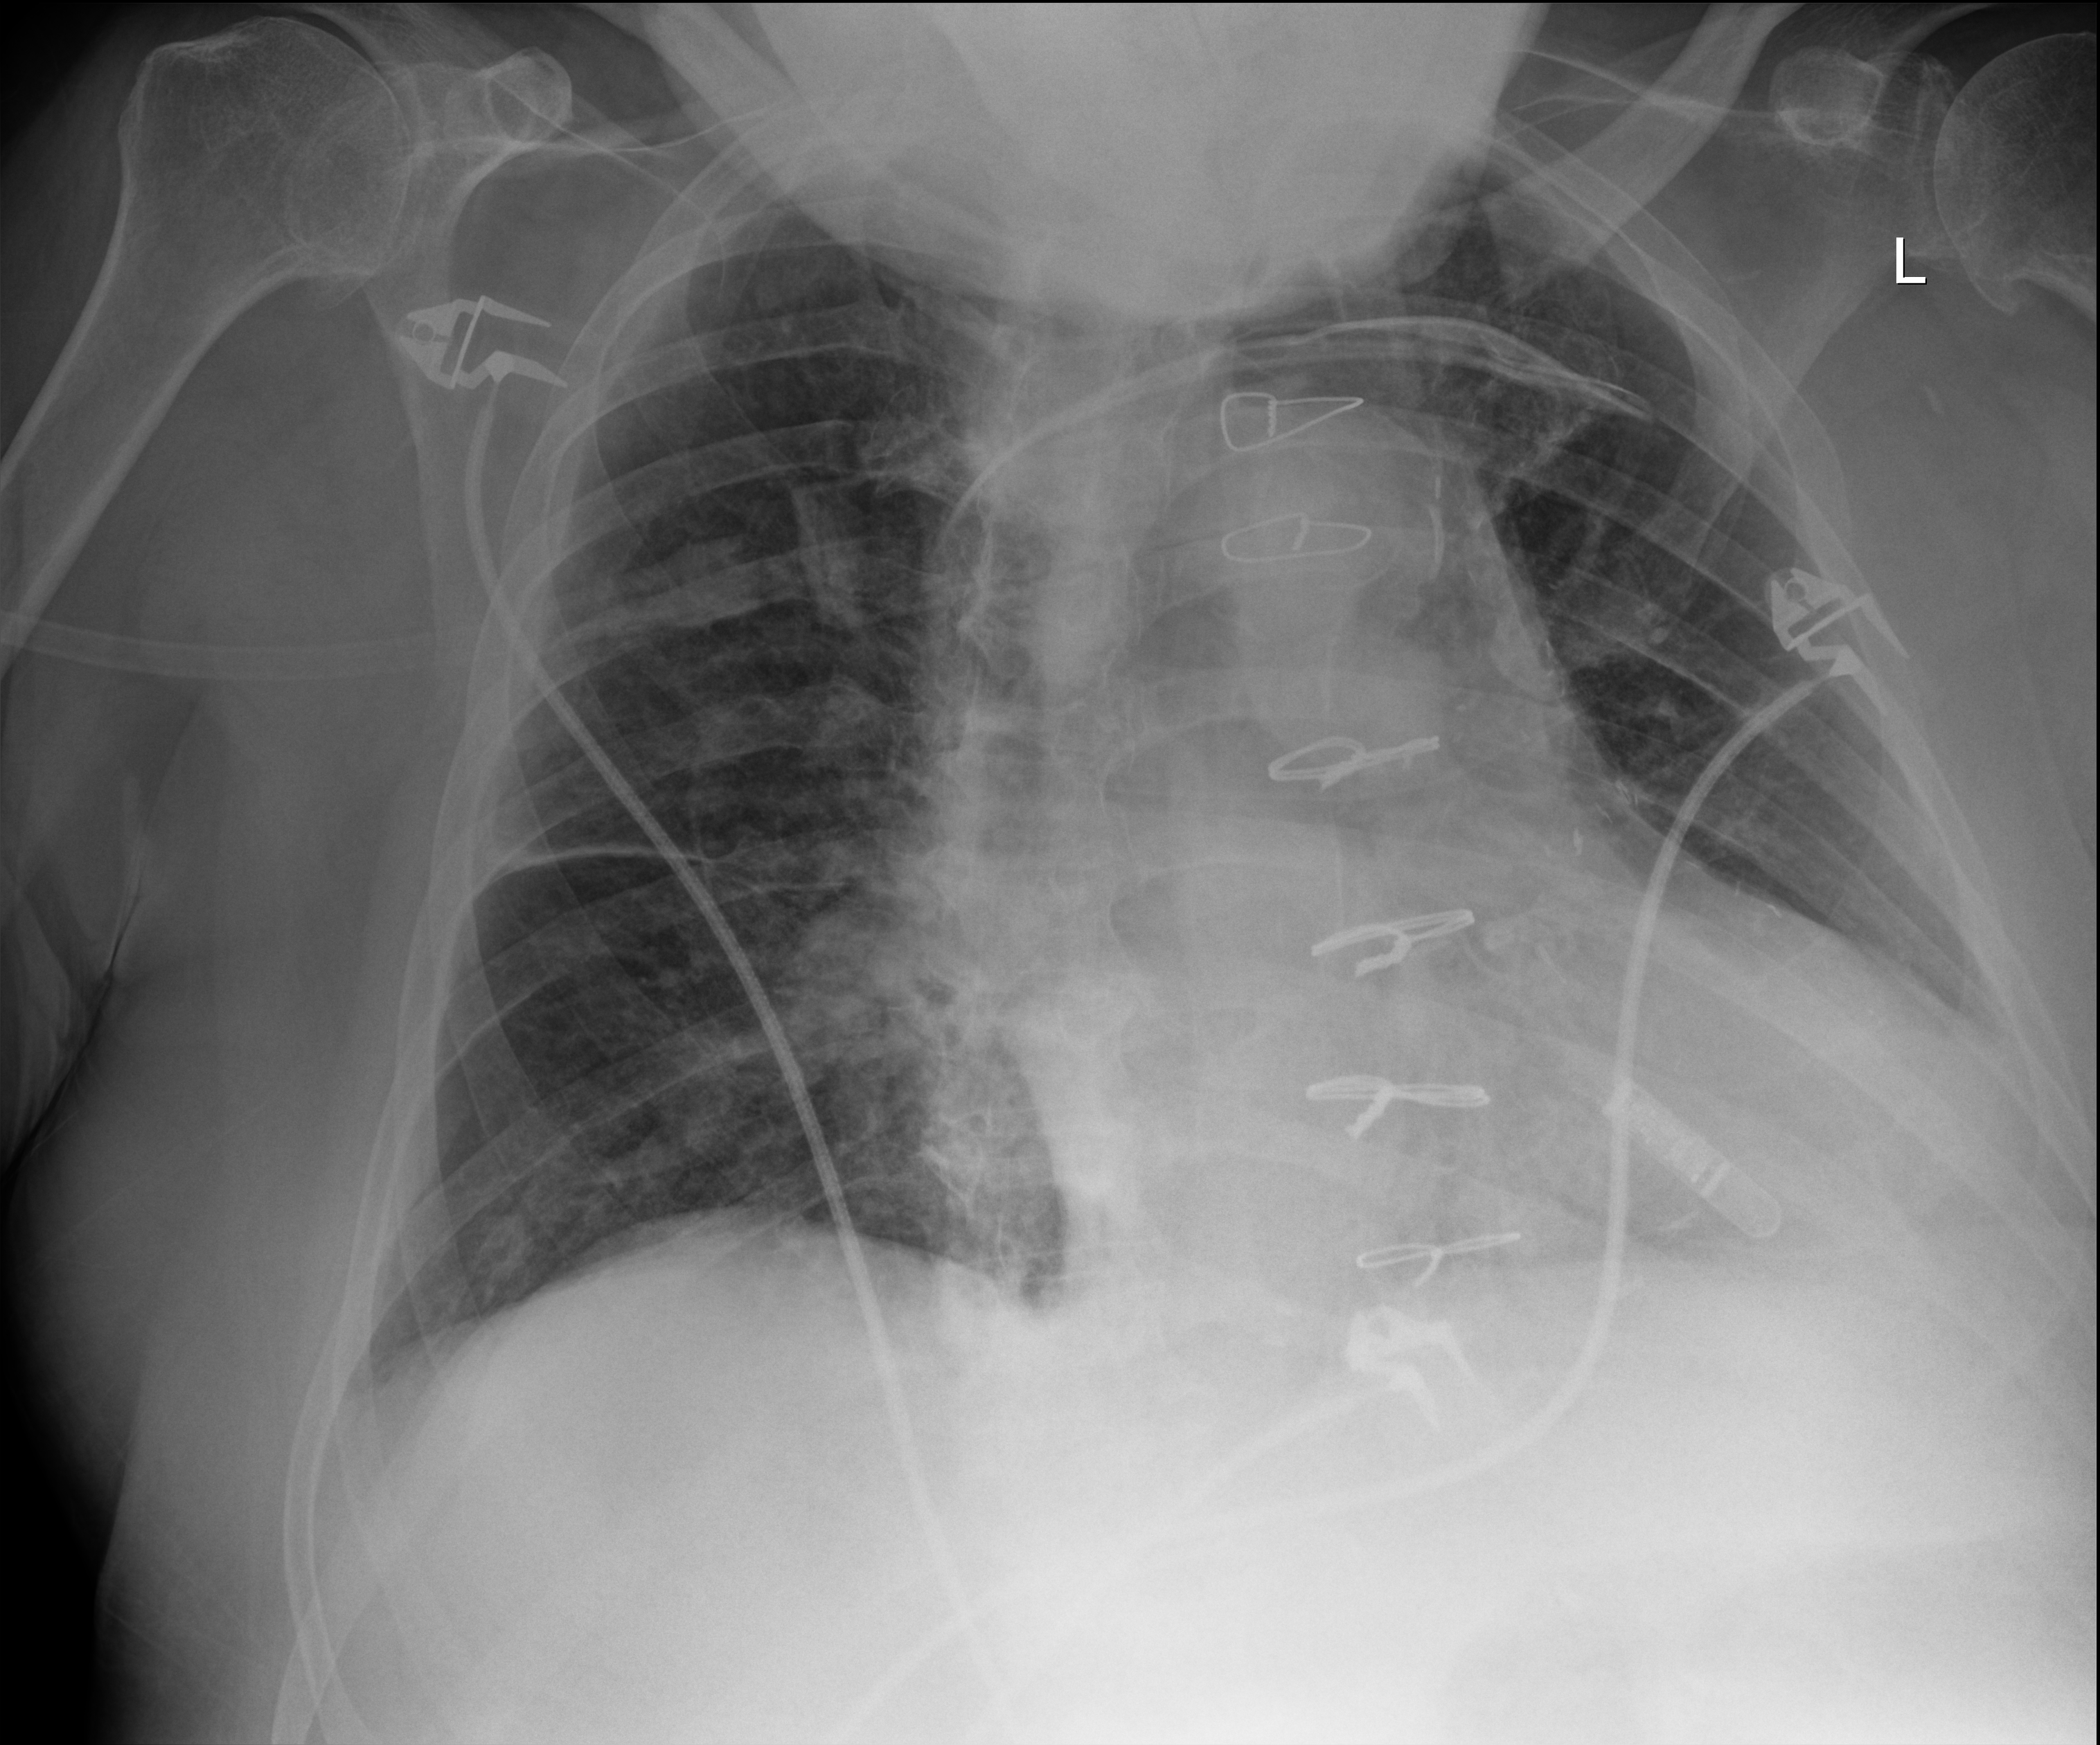
Chest X-ray (portable); anteroposterior (AP) projection. Male patient hospitalised with COVID-19, age 60–74 years.
Hospital-stay facts (about this admission, not read from this image; timing relative to this image not recorded): admitted to intensive care during this hospital stay: no; diabetes (admission record): no; mechanically ventilated during this hospital stay: no.